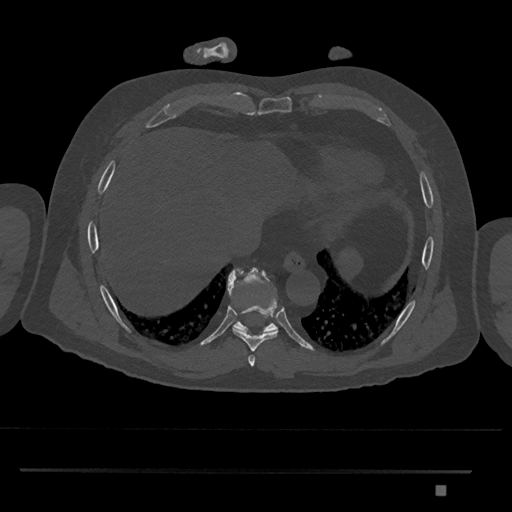
CT including the spine, one axial slice; slice 1090 of 1134 in the series (ordered by position); 120 kVp; bone window (W 1800 / L 400 HU); 0.5 mm slice thickness; 512 × 512 image matrix. Male patient, age 65 years. From the clinical record (not read from this slice): primary cancer: prostate.
Annotated regions visible in this slice (semi-automatic segmentation, software-assisted and operator-edited):
- T8 vertebra: bounding box [x1, y1, x2, y2] px = [233, 271, 278, 351]
- T9 vertebra: [227, 267, 278, 333]